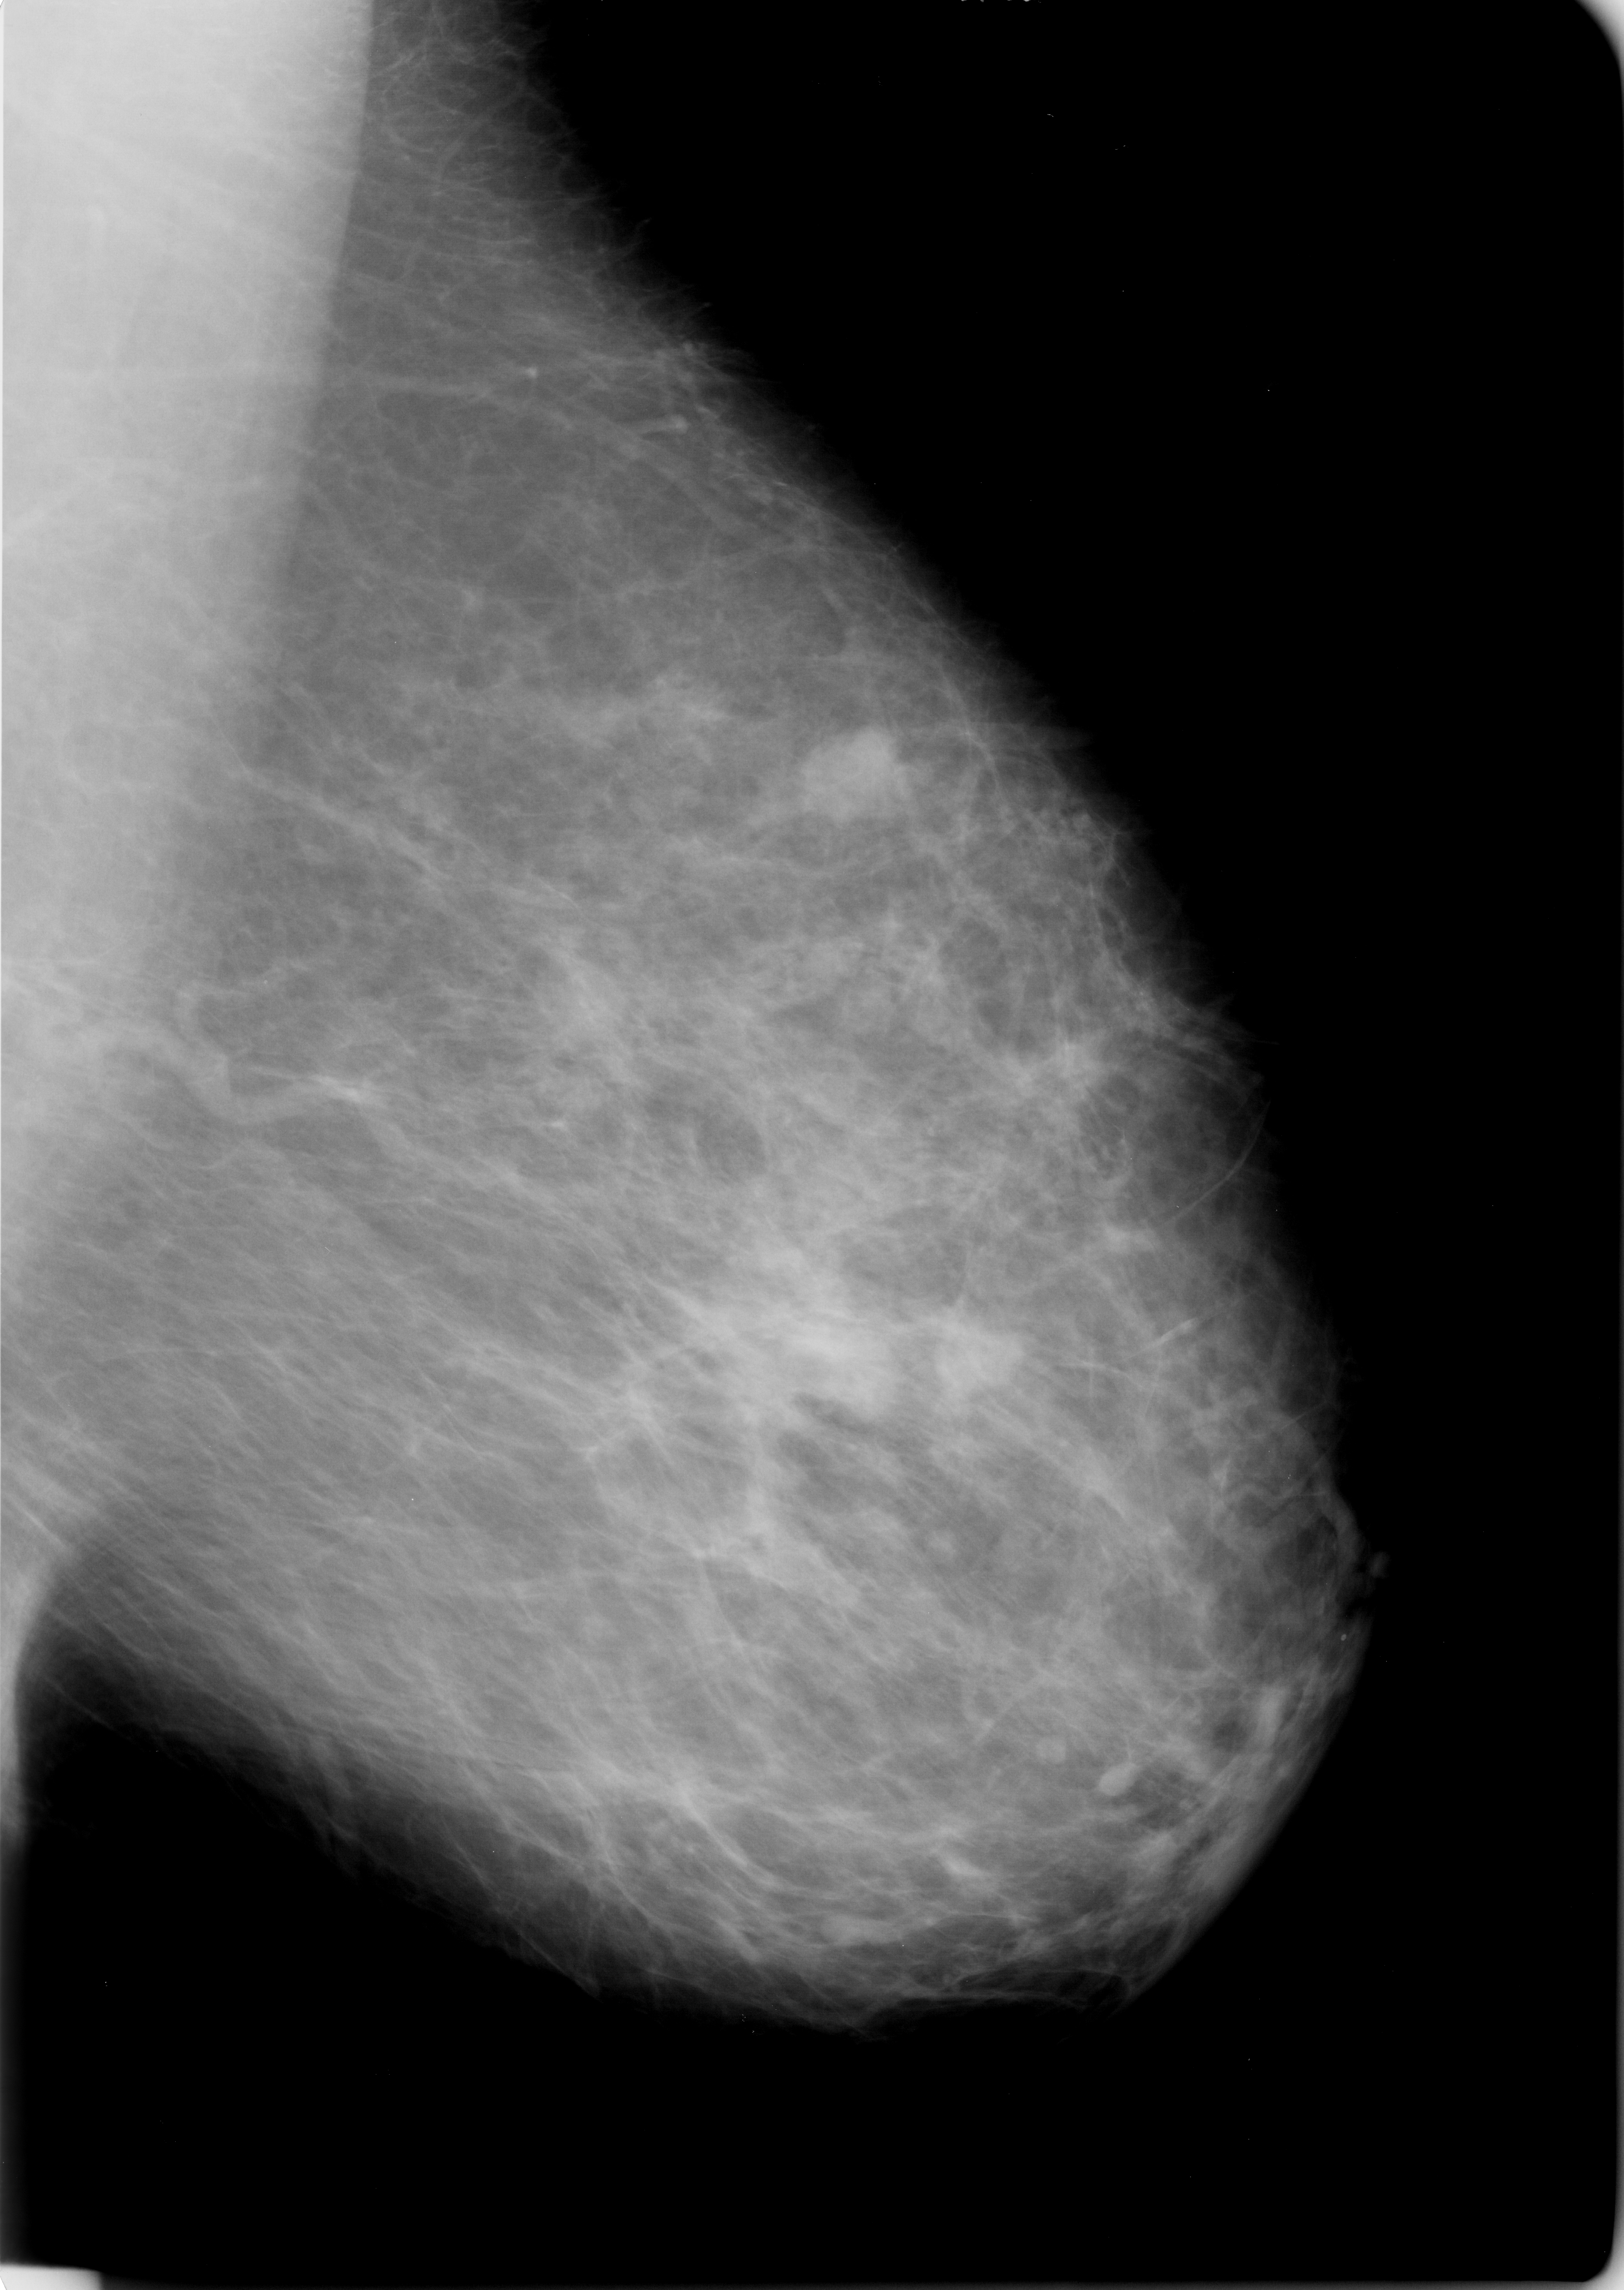
Digitized screen-film mammogram. Left breast. Mediolateral oblique (MLO) view. BI-RADS breast density category 3 (scale 1–4). 1624 × 2290 image matrix.
Marked abnormalities (boxes around the expert regions of interest):
- Finding 1 of 3: mass, shape lobulated, margins circumscribed / ill defined; BI-RADS assessment category 3; pathology result (as recorded, not read from the image): malignant: bounding box [x1, y1, x2, y2] px = [790, 1309, 897, 1418]
- Finding 2 of 3: mass, shape lobulated, margins circumscribed / ill defined; BI-RADS assessment category 3; subtlety rating 3 on a 1 (subtle) to 5 (obvious) scale; pathology result (as recorded, not read from the image): malignant: [809, 730, 900, 829]
- Finding 3 of 3: mass, shape lobulated, margins circumscribed / ill defined; BI-RADS assessment category 3; pathology result (as recorded, not read from the image): malignant: [930, 1300, 1027, 1402]